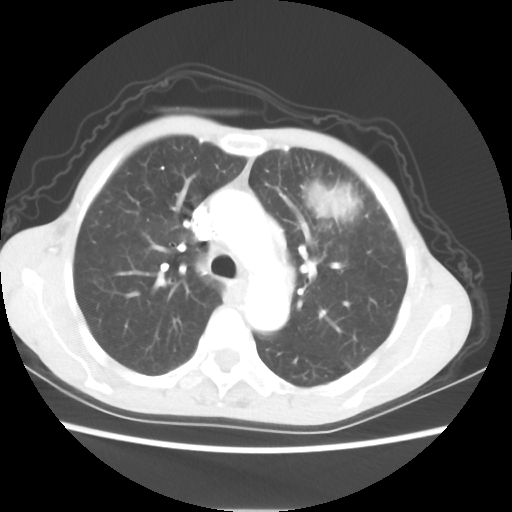
Chest CT, one axial slice. Position 40 of 56 along the scan axis. Reconstruction kernel STANDARD. 80 kVp. Lung window (W 1500 / L -600 HU). 5 mm slice thickness. 512 × 512 image matrix, field of view 331 × 331 mm. Patient: female, 60 years. Case-level facts recorded for this patient, not image findings: clinical TNM (as recorded): T4 N1 M0.
Outlined on this slice (bounding box drawn by a radiologist):
- lung tumour (recorded histology: adenocarcinoma): bounding box <316,179,357,225> (left, top, right, bottom; pixels)